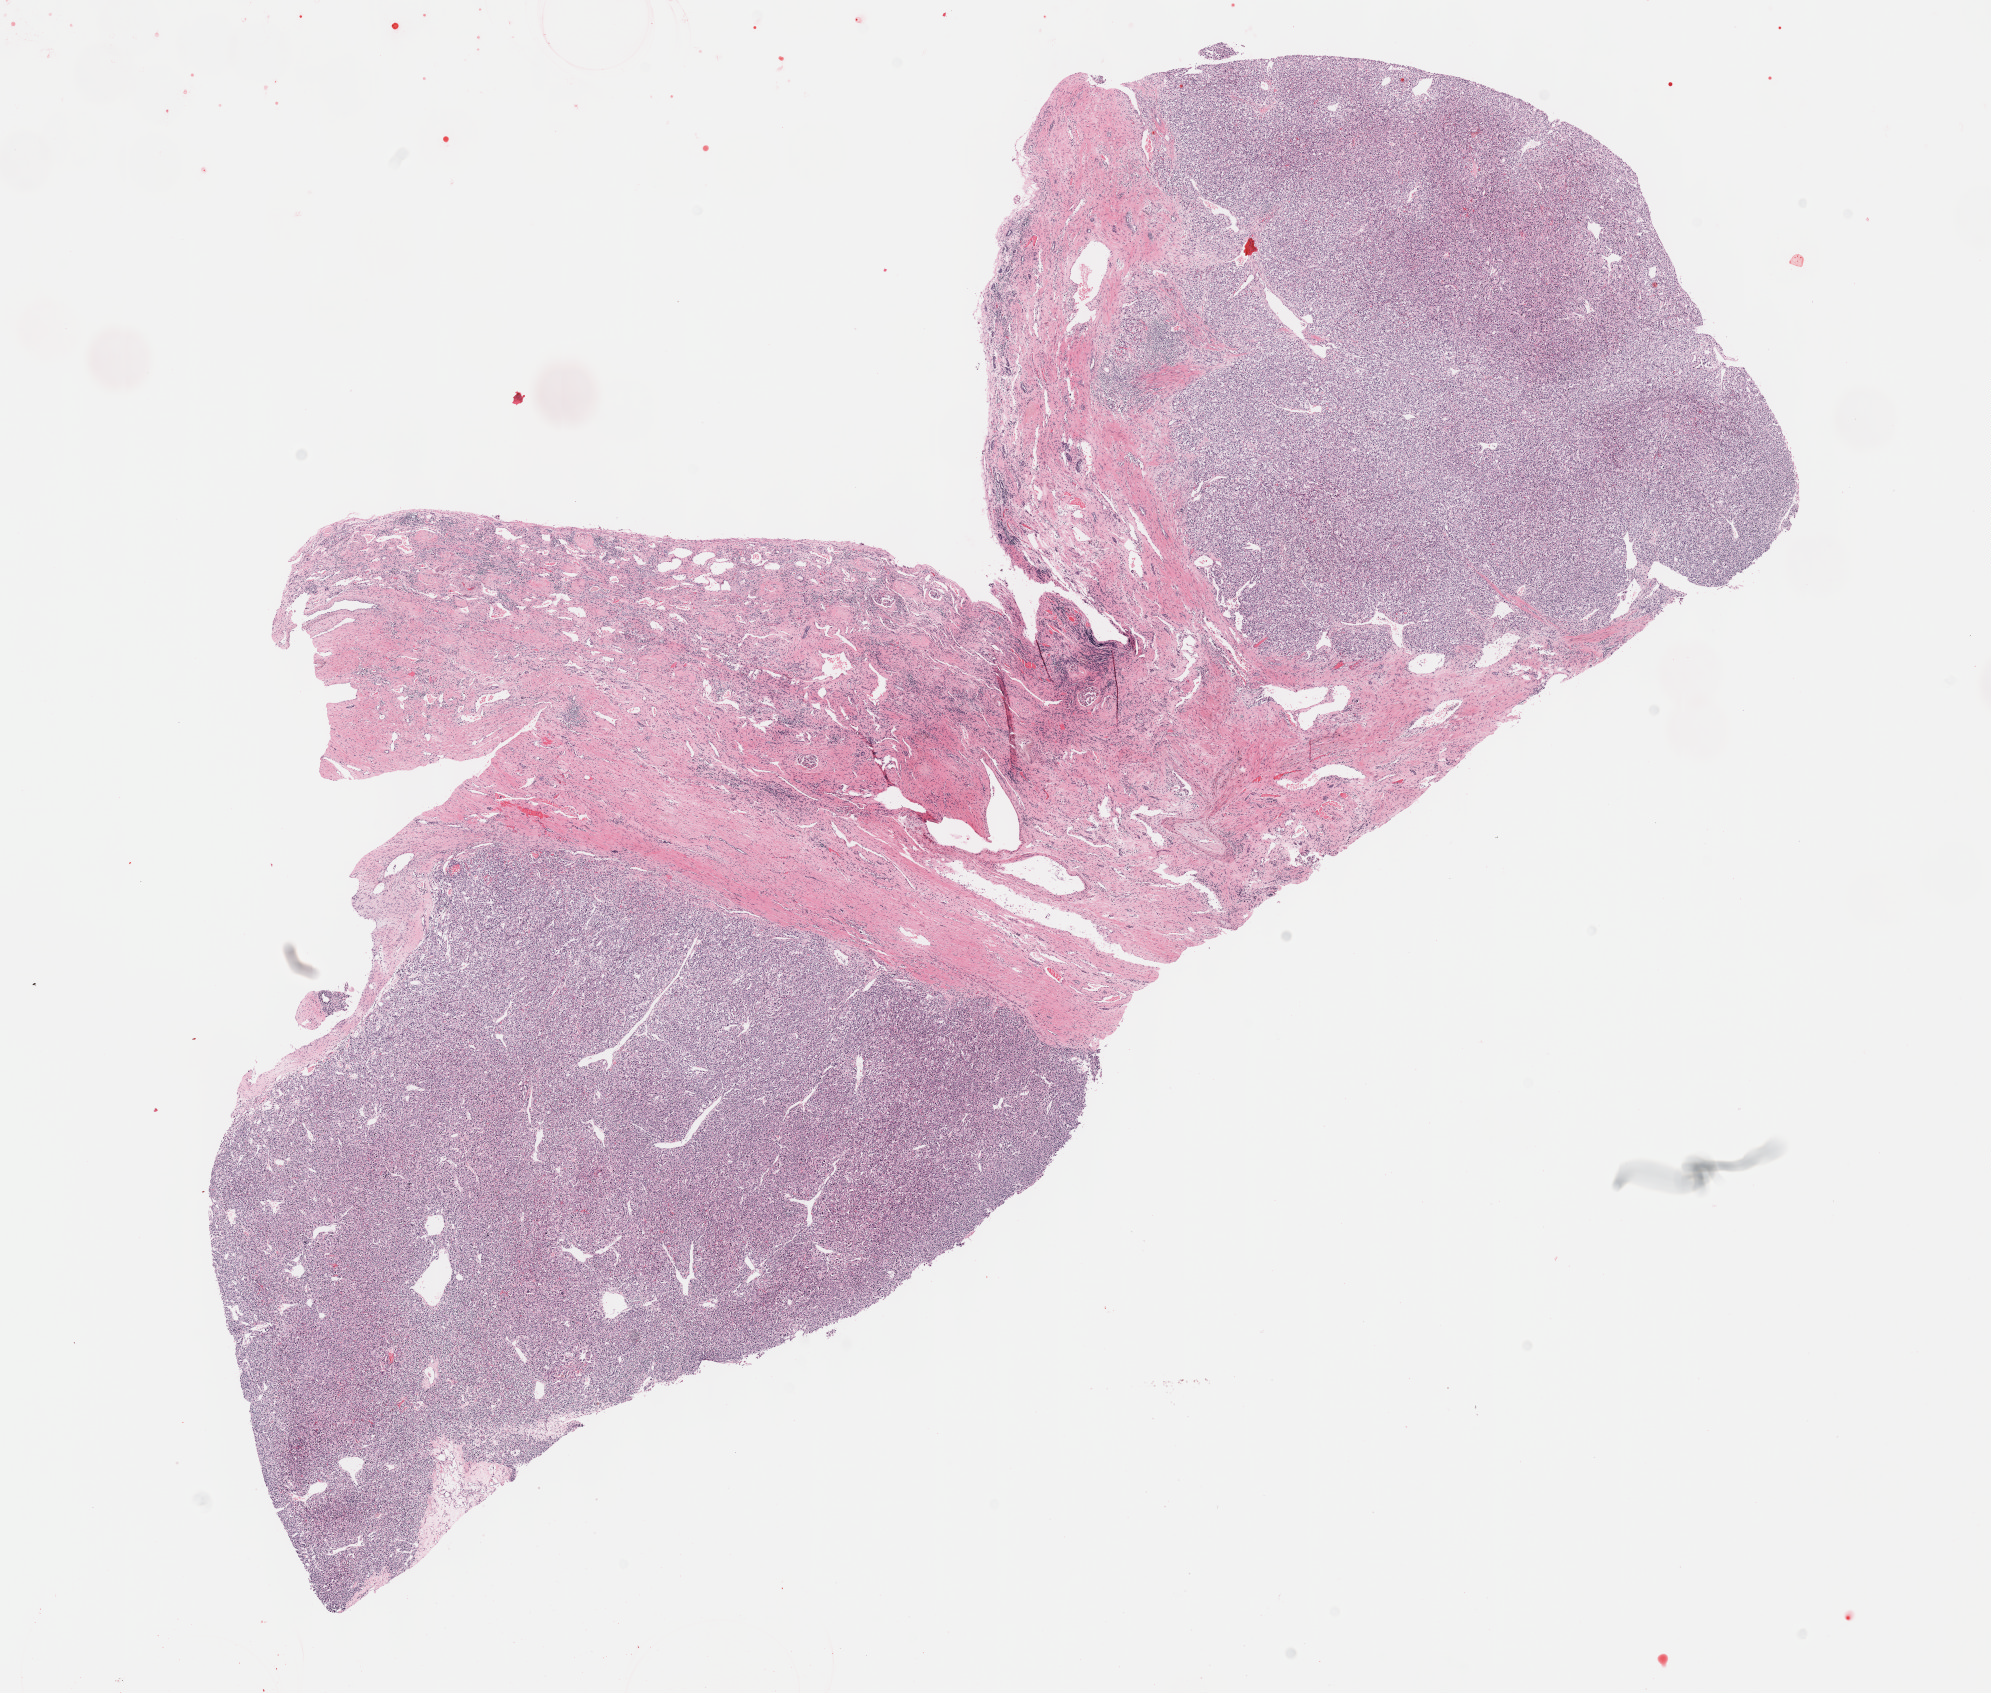
Hematoxylin and eosin (H&E) stained whole-slide image, whole scanned area (about 16.1 x 13.7 mm, slide scanned at 40x) shown as a low-resolution overview; FFPE section; primary tumour sample from the kidney. Patient: male, age at initial diagnosis 48 years. Histologic grade: G3 (poorly differentiated).
* TNM: T1b NX M0
* diagnosis: Clear cell adenocarcinoma, NOS
* AJCC pathologic stage: I